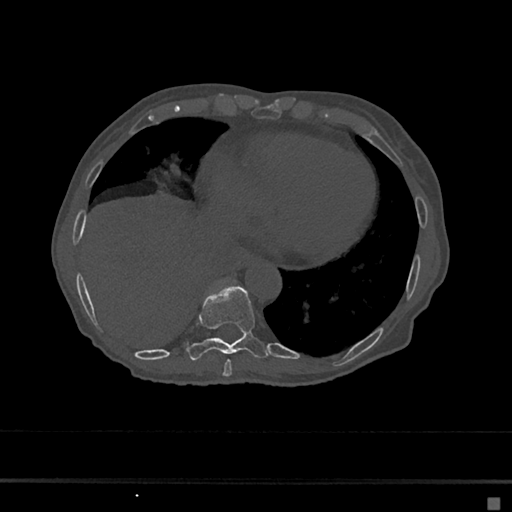
CT including the spine, one axial slice; position 274 of 797 along the scan axis; reconstruction kernel Br40s/3; bone window (W 1800 / L 400 HU); 0.5 mm slice thickness; 512 × 512 image matrix, field of view 360 × 360 mm. Female patient, age 68 years. From the clinical record (not read from this slice): primary cancer: renal.
Structures marked on this image (semi-automatically segmented with operator editing):
- T8 vertebra: box from (x=223, y=359) to (x=232, y=377) px
- T9 vertebra: (x=186, y=284)–(x=271, y=361)